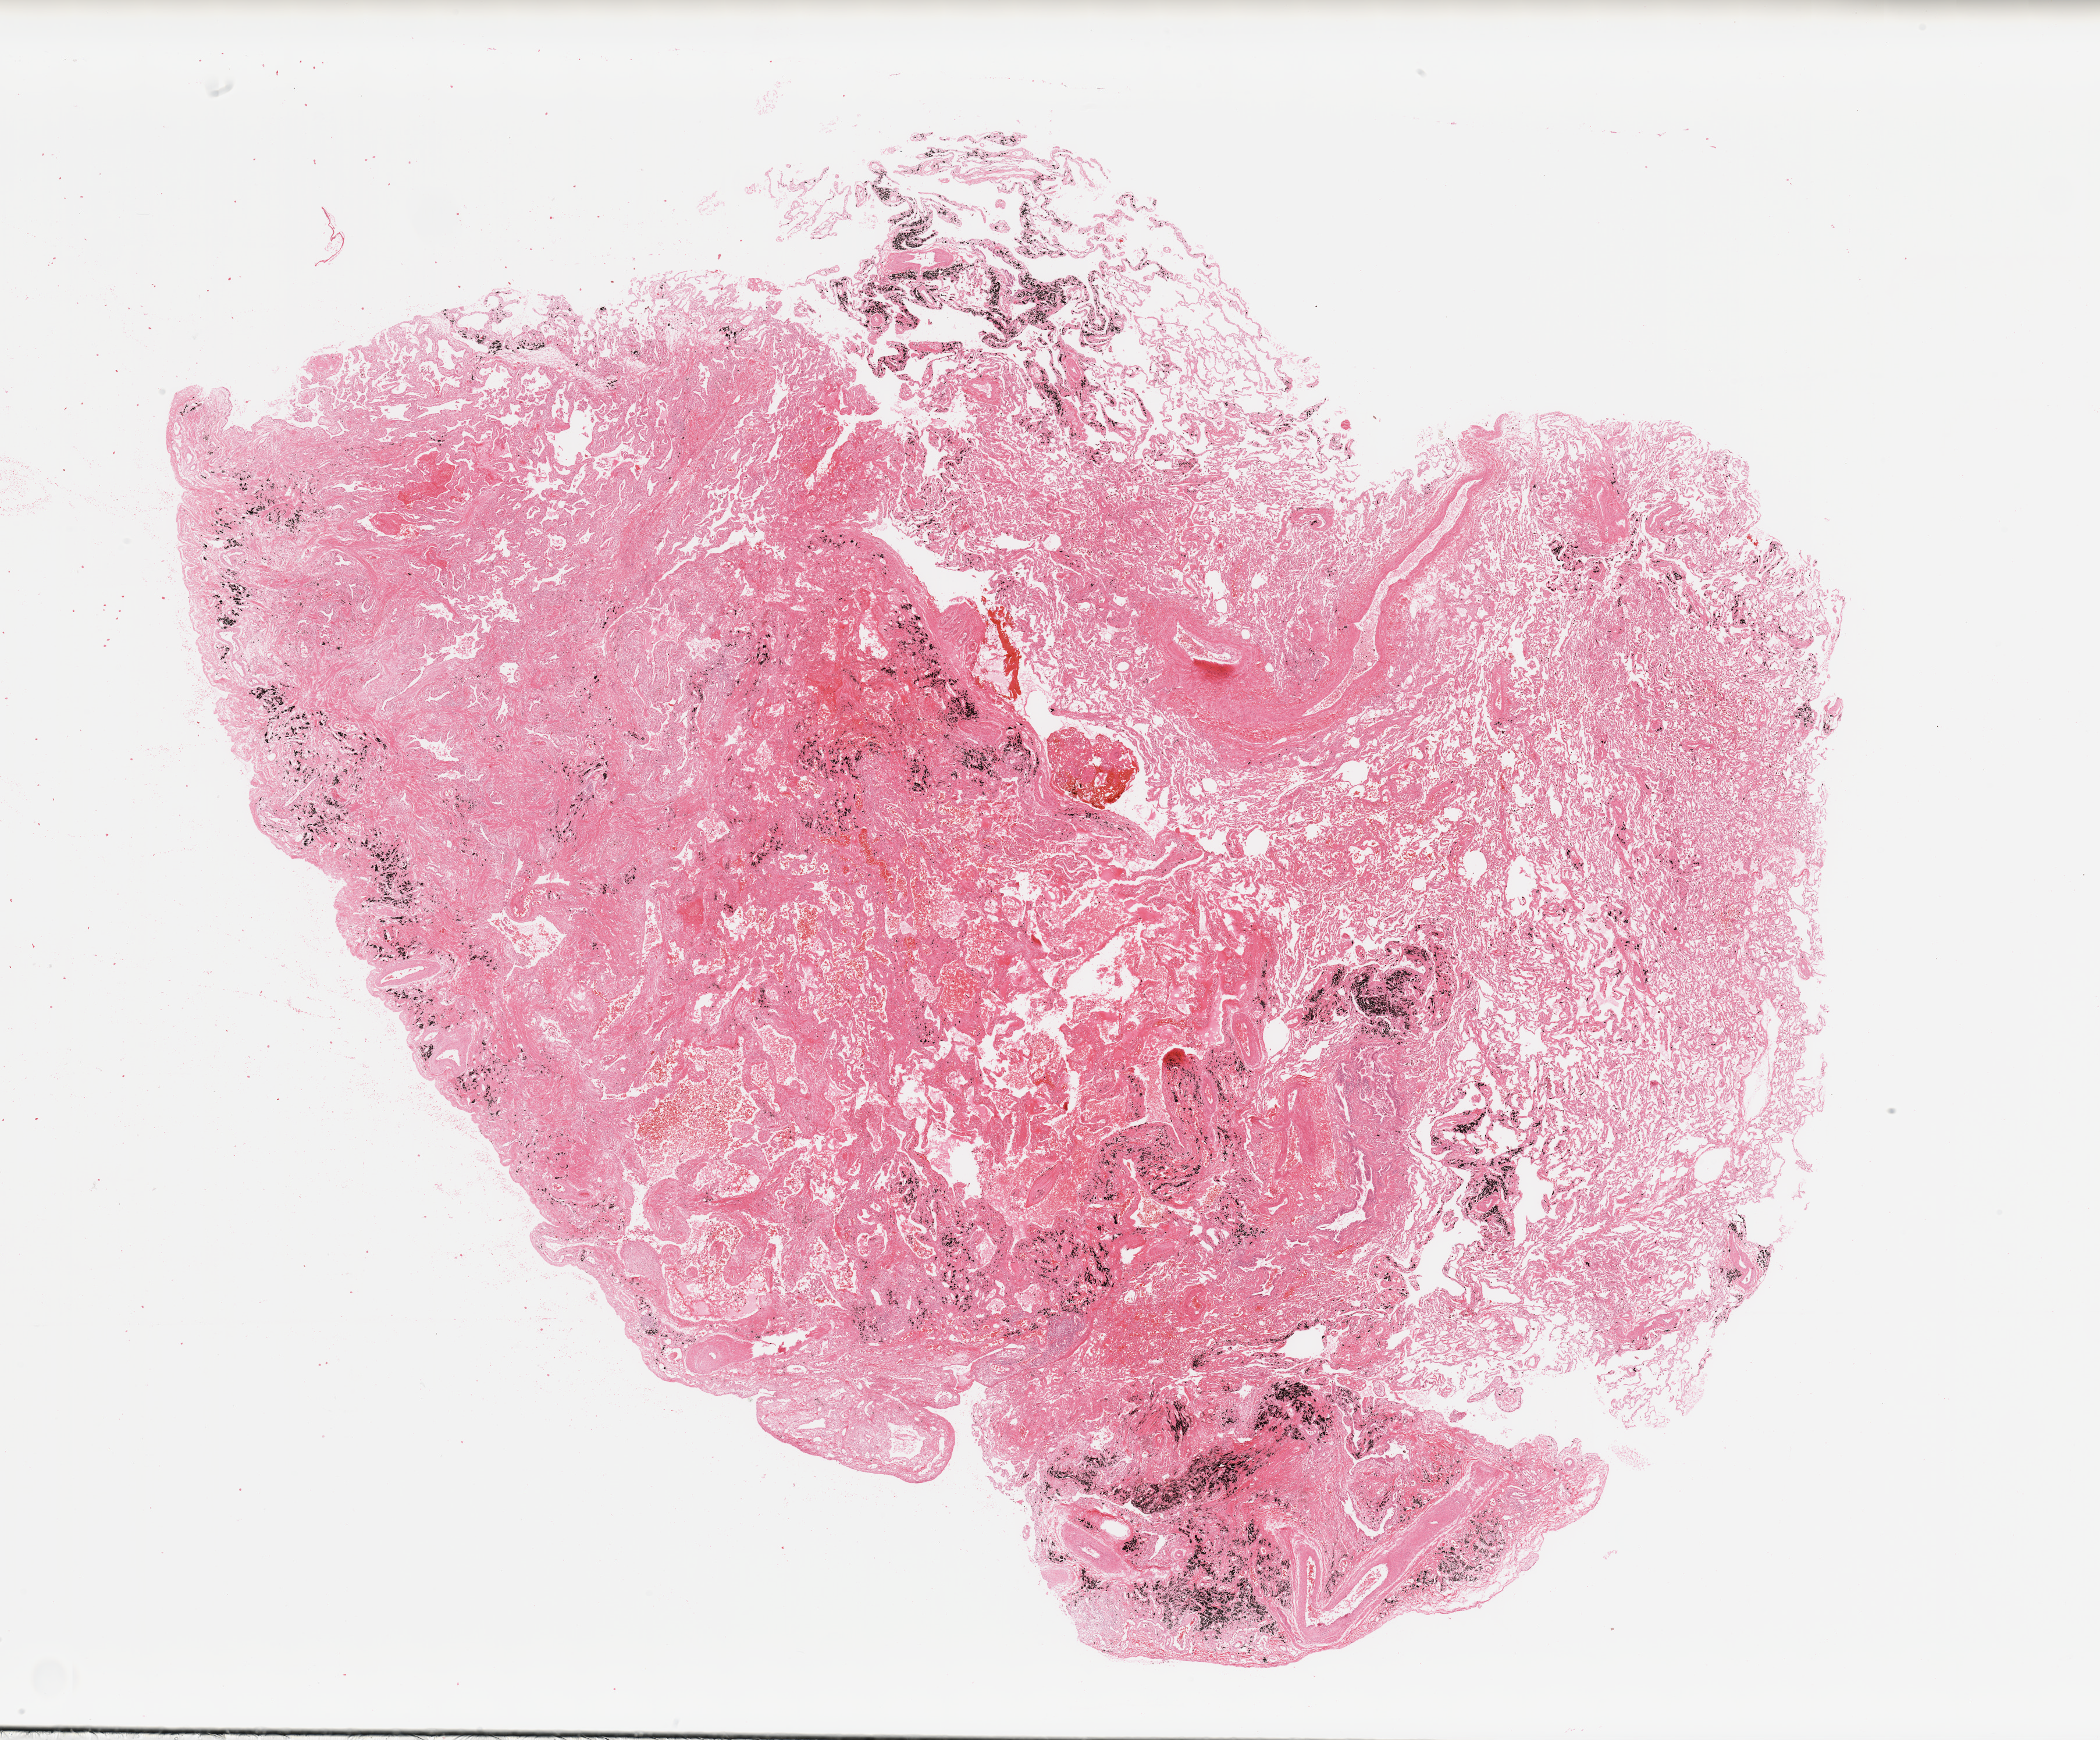
Digitized H&E tissue section (whole slide) — shown as a low-resolution overview of the whole scanned area (about 28.5 x 23.7 mm, from a 20x scan), lung, normal (non-tumour) tissue. Patient: male, age 54 years.
This section: normal (non-tumour) tissue from the same patient. Patient diagnosis: Adenocarcinoma, NOS.